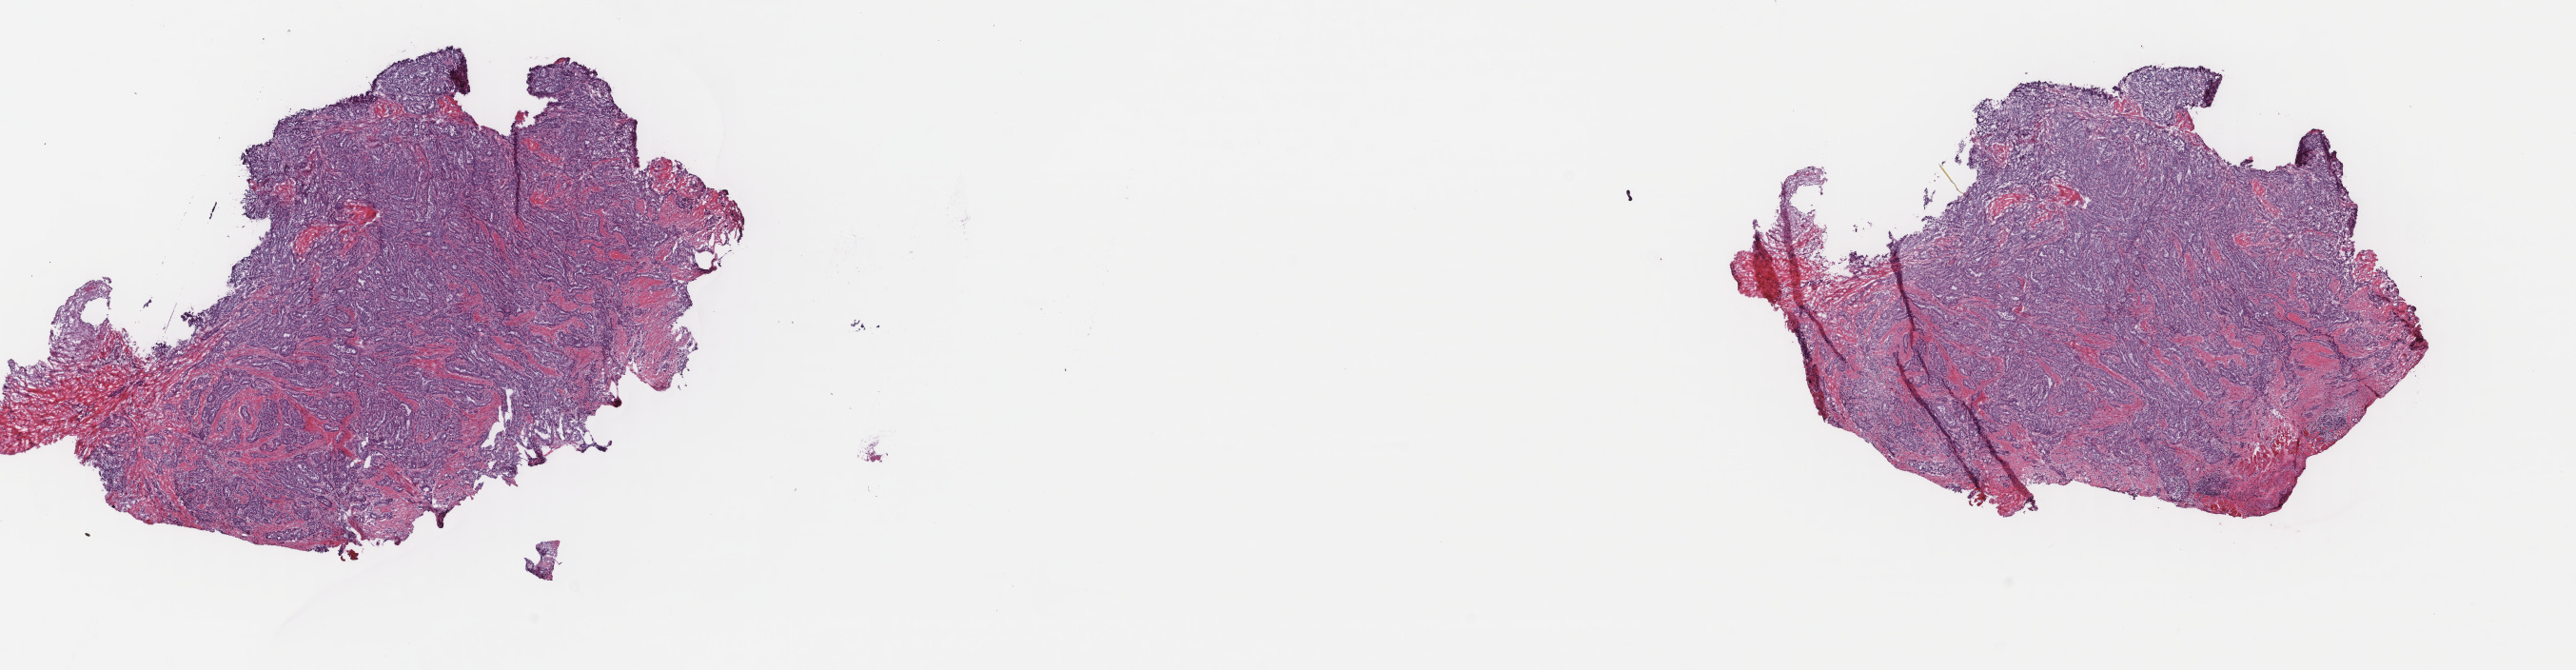
Whole-slide histology image, H&E, a low-resolution overview of the entire scanned area, about 21.5 x 5.6 mm, frozen section from the top of the tissue portion, primary tumour sample from the thyroid. Female patient; age at initial diagnosis 54 years. Slide review estimates, as recorded: tumour cells 100%, tumour nuclei 85%, normal cells 0%, stromal cells 0%, necrosis 0%. Infiltration values recorded for this section: lymphocyte infiltration 0%, monocyte infiltration 0%, neutrophil infiltration 0%.
Diagnosis: Papillary adenocarcinoma, NOS (thyroid gland). TNM: T3 N0 MX. AJCC pathologic stage: III. Lymph nodes positive (case pathology): 0 of 7 examined.